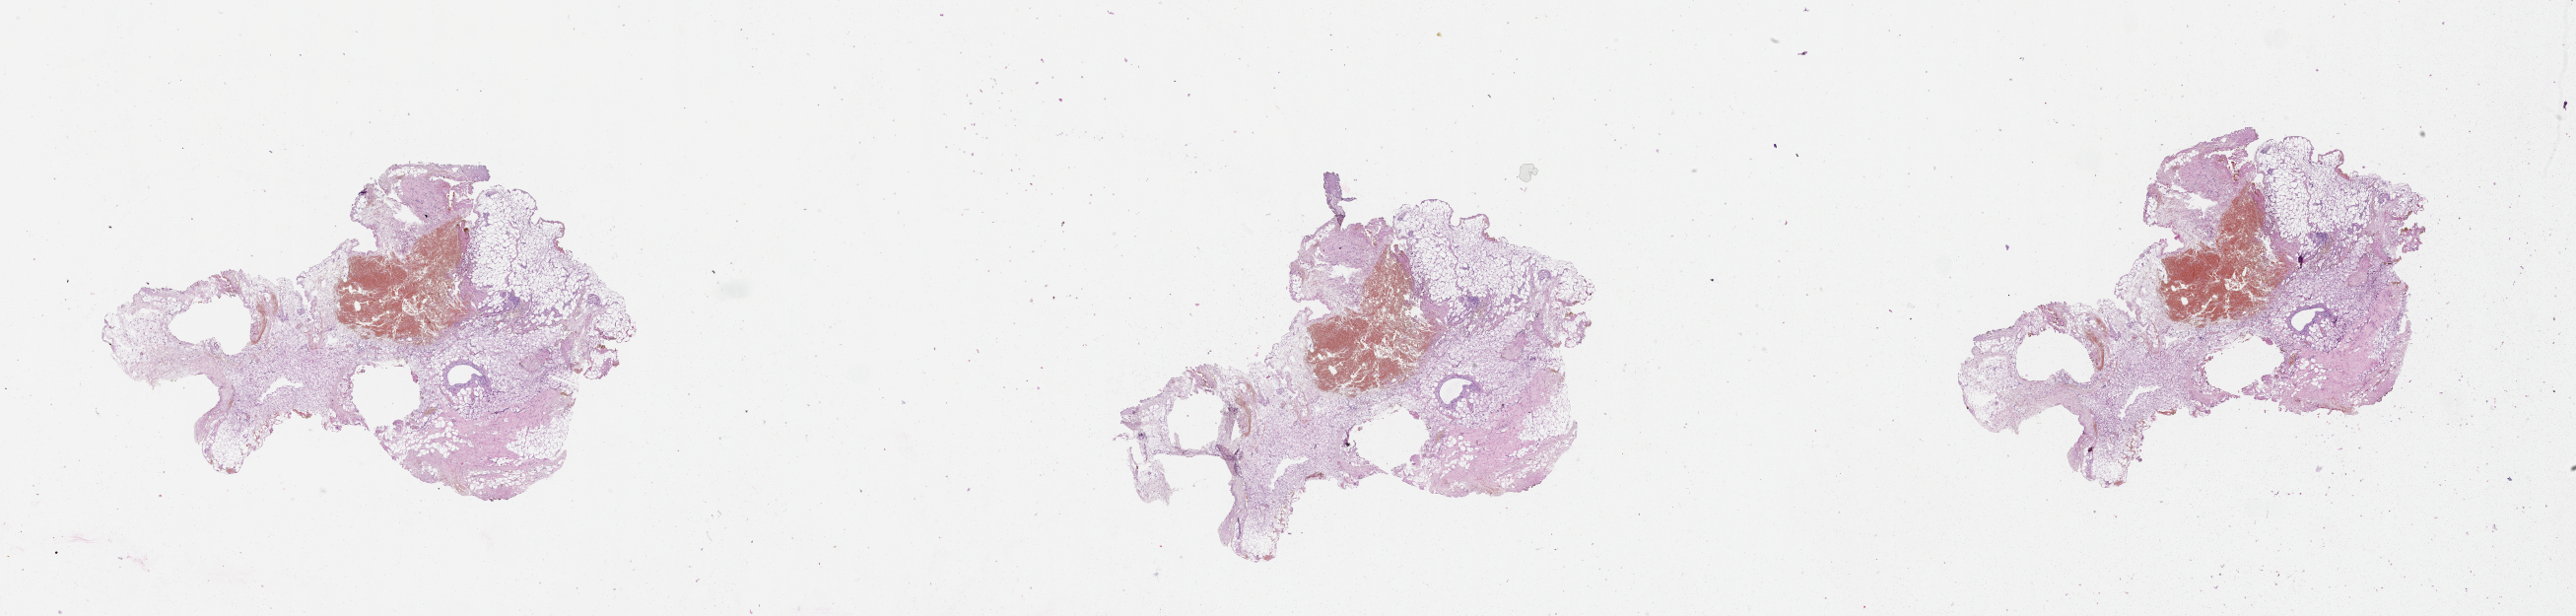
Whole-slide histology image, H&E — a low-resolution overview of the entire scanned area, about 42.1 x 10.1 mm (from a 20x scan). 83-year-old male patient.
Patient diagnosis: Malignant melanoma, NOS.